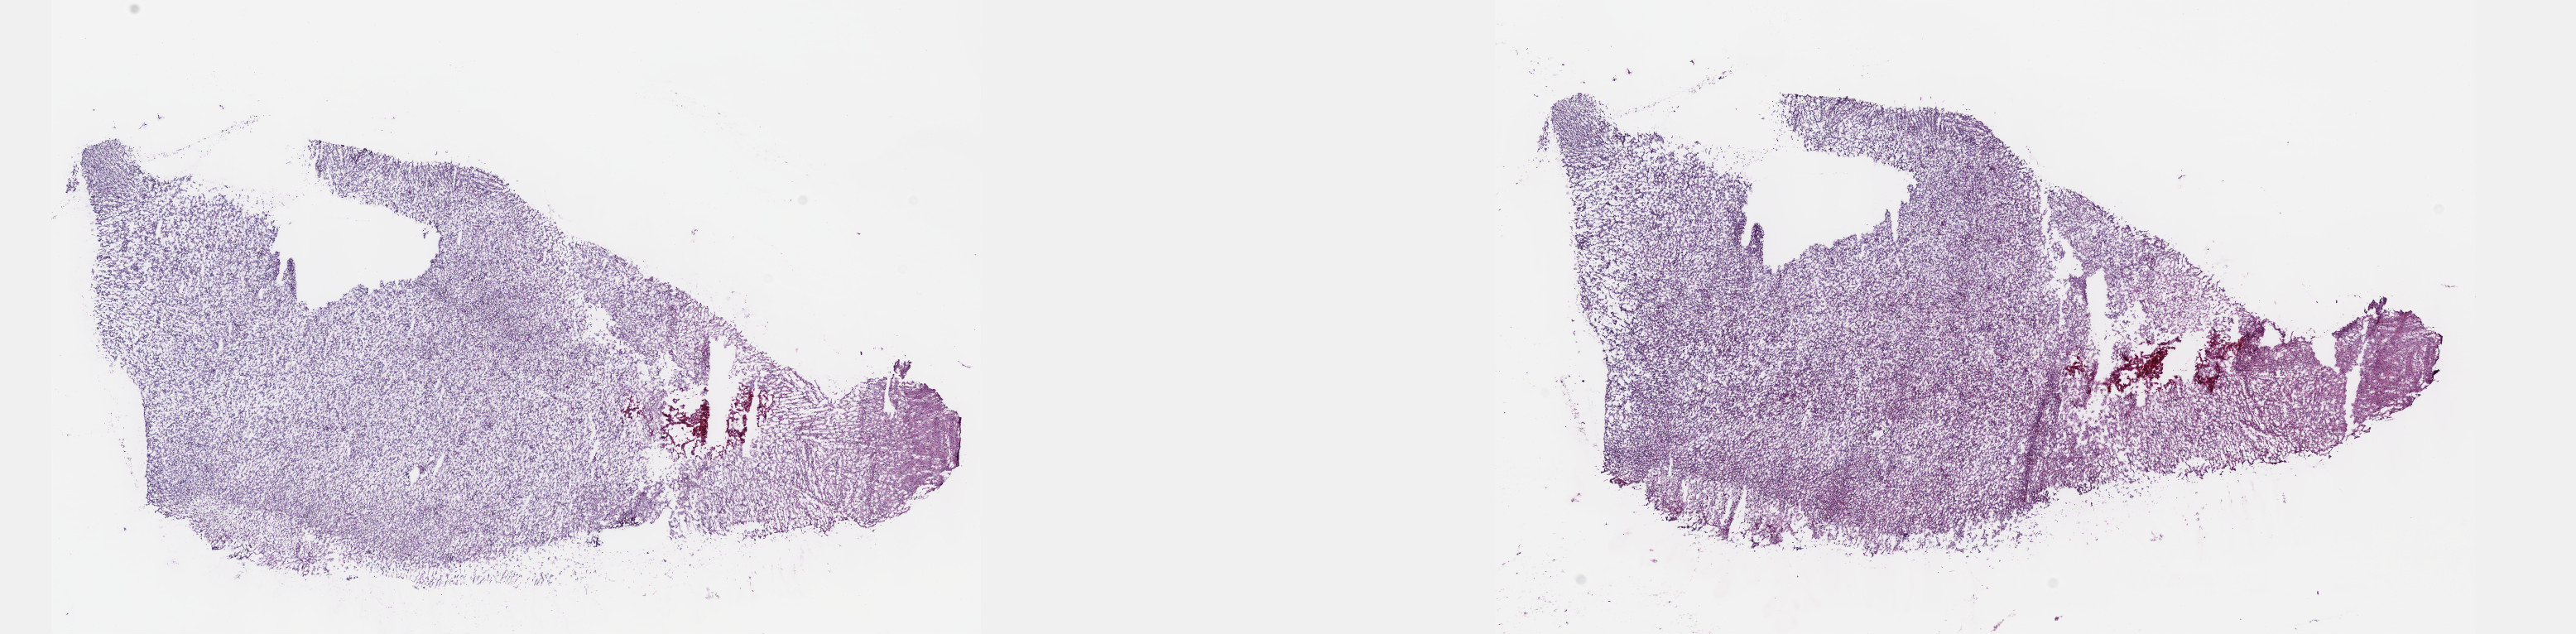
Digitized H&E tissue section (whole slide) — low-resolution overview of the scanned area, about 25.1 x 6.2 mm (slide scanned at 40x). Frozen section from the top of the tissue portion. Sample: primary tumour, brain. Female patient; age at initial diagnosis 37 years. Histologic grade: G3 (poorly differentiated). Composition of this section per pathologist review: tumour cells 60%, tumour nuclei 90%, normal cells 10%, stromal cells 30%, necrosis 0%. Infiltration values recorded for this section: lymphocyte infiltration 0%, monocyte infiltration 0%, neutrophil infiltration 0%.
Histologic diagnosis: Astrocytoma, anaplastic (cerebrum).